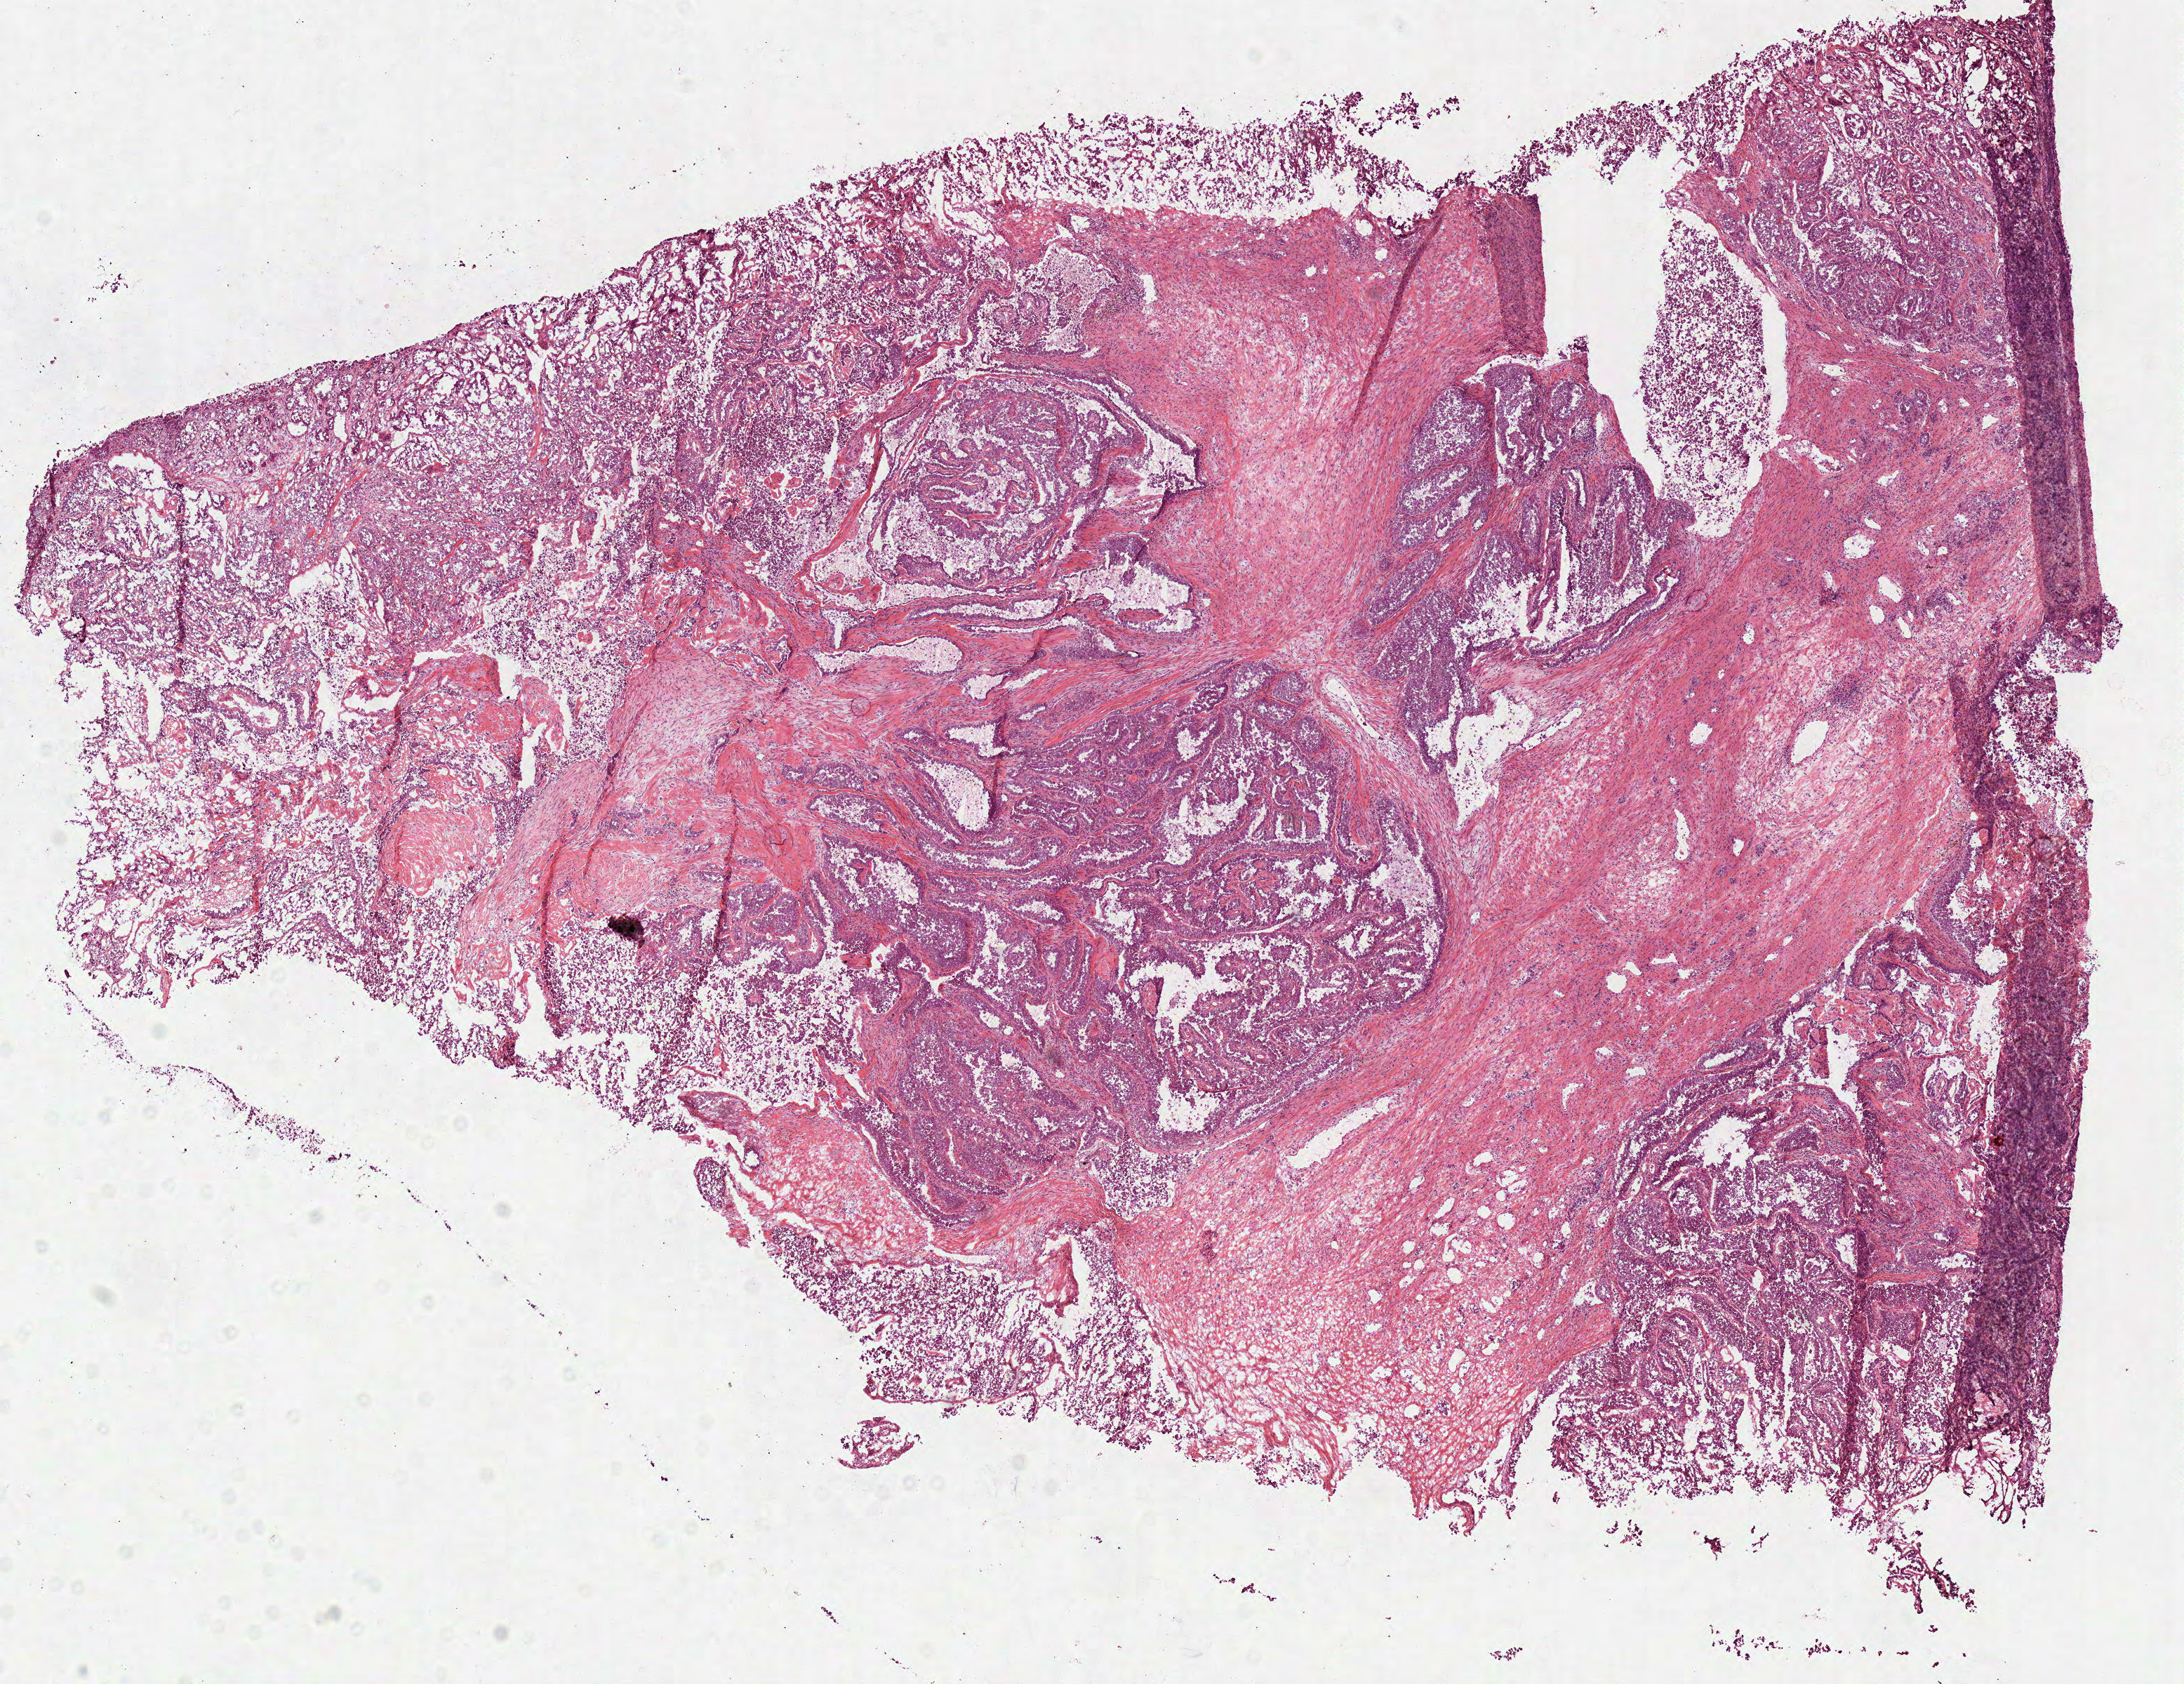
Whole-slide histology image, H&E-stained, whole scanned area (about 12.2 x 9.4 mm, acquisition: 40x scan) shown as a low-resolution overview; frozen section; primary tumour sample from the kidney. Female patient; age at initial diagnosis 60 years. Pathologist review of this section (percent, as recorded): tumour cells 70%, tumour nuclei 80%, normal cells 0%, stromal cells 30%, necrosis 0%.
* AJCC pathologic stage: IV
* histologic diagnosis: Papillary adenocarcinoma, NOS